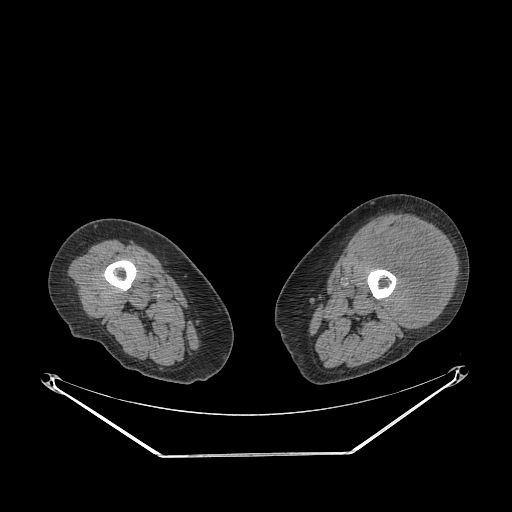
CT of an extremity soft-tissue mass (from a PET/CT study), one axial slice. Slice 213 of 267 in the series (ordered by position). Reconstruction kernel STANDARD. 140 kVp. Soft-tissue window (W 400 / L 40 HU). 512 × 512 image matrix. Female patient. From the clinical record (not read from this slice): histological type: undifferentiated – high grade; grade: high; site of the primary tumour: left thigh.
Annotated regions visible in this slice (expert contour drawn on MRI and transferred to this co-registered scan by the dataset authors):
- gross tumour volume including surrounding oedema: bounding box [x1, y1, x2, y2] px = [363, 224, 449, 328]
- gross tumour volume (mass): [368, 230, 449, 328]